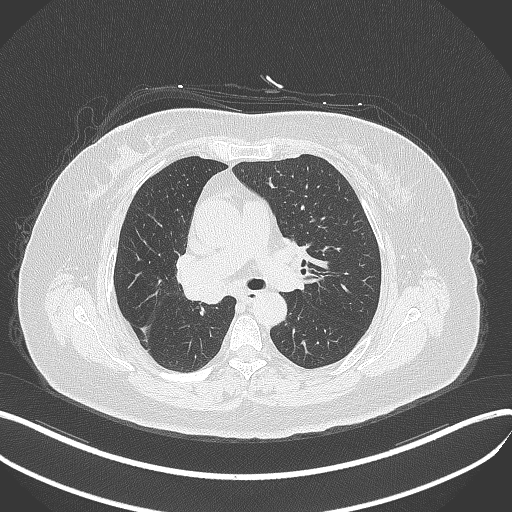
Chest CT, one axial slice; slice 218 of 376 in the series (ordered by position); 120 kVp; lung window (W 1500 / L -600 HU); 1 mm slice thickness; 512 × 512 image matrix, field of view 400 × 400 mm. Patient: female, 60 years. Case-level facts recorded for this patient, not image findings: clinical TNM (as recorded): T1c N0 M0.
Structures marked on this image (bounding box drawn by a radiologist):
- lung tumour (recorded histology: squamous cell carcinoma): box from (x=181, y=274) to (x=228, y=309) px